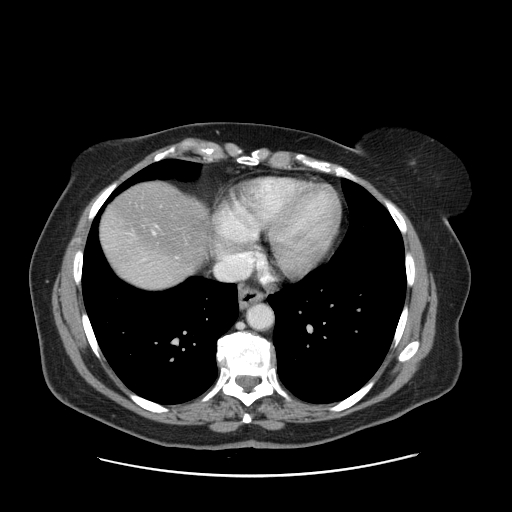
Contrast-enhanced abdominal CT, one axial slice; slice 144 of 161 in the series (ordered by position); intravenous contrast given; soft-tissue window (W 400 / L 40 HU); 512 × 512 image matrix, field of view 398 × 398 mm. Female patient, age 62 years. From the clinical record (not read from this slice): diagnosis: colorectal cancer liver metastases, imaged before liver resection; multiple liver metastases: no; largest metastasis: 2.5 cm.
Structures marked on this image (manually delineated by an expert):
- hepatic veins: bounding box <131,232,156,235> (left, top, right, bottom; pixels)
- liver: <100,183,208,288>
- planned liver remnant (the part of the liver to remain after resection): <102,183,208,271>